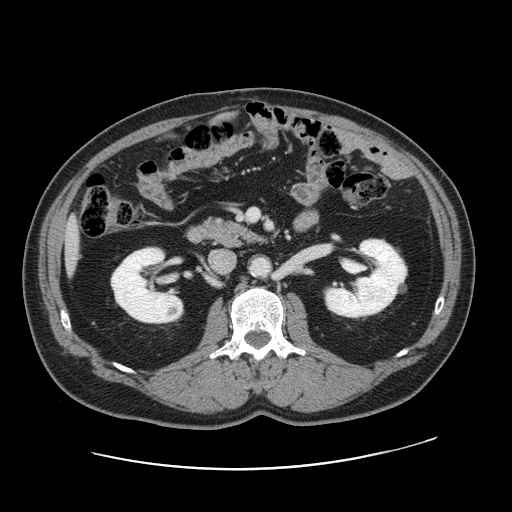
Contrast-enhanced abdominal CT, one axial slice. Position 64 of 178 along the scan axis. Soft-tissue window (W 400 / L 40 HU). 2.5 mm slice thickness. 512 × 512 image matrix, field of view 403 × 403 mm. Male patient, age 63 years. From the clinical record (not read from this slice): diagnosis: colorectal cancer liver metastases, imaged before liver resection; multiple liver metastases: yes; largest metastasis: 8 cm; disease in both lobes: yes.
Outlined on this slice (expert manual segmentation):
- liver: box from (x=65, y=224) to (x=79, y=261) px